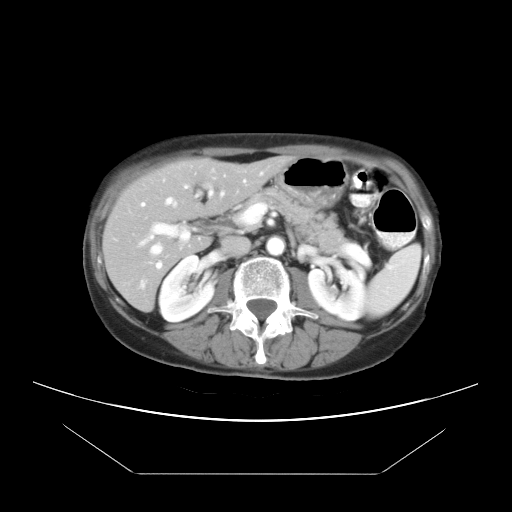
Contrast-enhanced abdominal CT, one axial slice. Slice 10 of 21 in the series (ordered by position). Intravenous contrast given. Soft-tissue window (W 400 / L 40 HU). 7.5 mm slice thickness. 512 × 512 image matrix, field of view 392 × 392 mm. Female patient, age 72 years. From the clinical record (not read from this slice): diagnosis: colorectal cancer liver metastases, imaged before liver resection; multiple liver metastases: yes.
Annotated regions visible in this slice (manually delineated by an expert):
- hepatic veins: bounding box <138,197,177,256> (left, top, right, bottom; pixels)
- liver: <104,158,287,310>
- planned liver remnant (the part of the liver to remain after resection): <104,158,287,289>
- portal vein (with intrahepatic branches): <140,190,224,268>